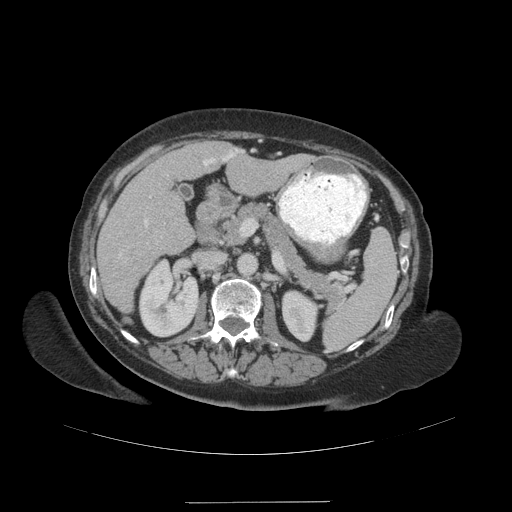
Contrast-enhanced abdominal CT (liver protocol), one axial slice. Slice 54 of 99 in the series (ordered by position). Soft-tissue window (W 400 / L 40 HU). 2.5 mm slice thickness. 512 × 512 image matrix, field of view 440 × 440 mm. Case-level facts recorded for this patient, not image findings: diagnosis: hepatocellular carcinoma (patient treated with transarterial chemoembolisation; whether this scan precedes or follows treatment is not stated here); TNM stage (as recorded): Stage-IVA; Child-Pugh class: A; tumour nodularity: multinodular.
Outlined on this slice (semi-automatically segmented with operator editing):
- liver parenchyma outside the tumour (the mass and vessels are separate outlines, so this box may not span the whole liver): bounding box [x1, y1, x2, y2] px = [96, 140, 310, 312]
- liver vessels: [119, 149, 243, 257]